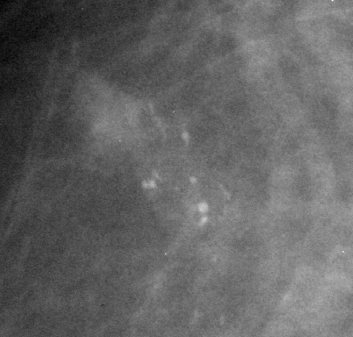
Crop from a digitized film mammogram around one marked abnormality, right breast, MLO view.
- Marked abnormality: calcifications, morphology pleomorphic, distribution clustered; BI-RADS assessment category 5; pathology (as recorded): malignant.